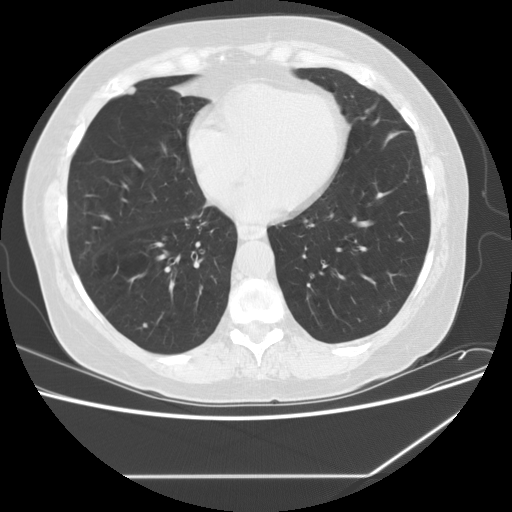
Low-dose screening chest CT, axial slice, second screening round (one year after baseline), lung window (W 1500 / L -600 HU), 2.5 mm slice thickness, standard (soft-tissue) reconstruction kernel (STANDARD), 512 × 512 image matrix, field of view 360 × 360 mm. Female participant, aged 59 years at enrolment. Current smoker at enrolment.
- Expert reader's lesion annotation, bounding box <124,310,164,346> (left, top, right, bottom; pixels).
- No non-calcified nodule or mass ≥4 mm was recorded by the screening reader at this exam.
- Official screen result: negative screen, significant abnormalities not suspicious for lung cancer.
- Later outcome: lung cancer diagnosed 380 days after this screen (after the third annual screen) — non-small cell carcinoma, right lower lobe, poorly differentiated (G3), stage IA (AJCC 6th edition), 15 mm at pathology.